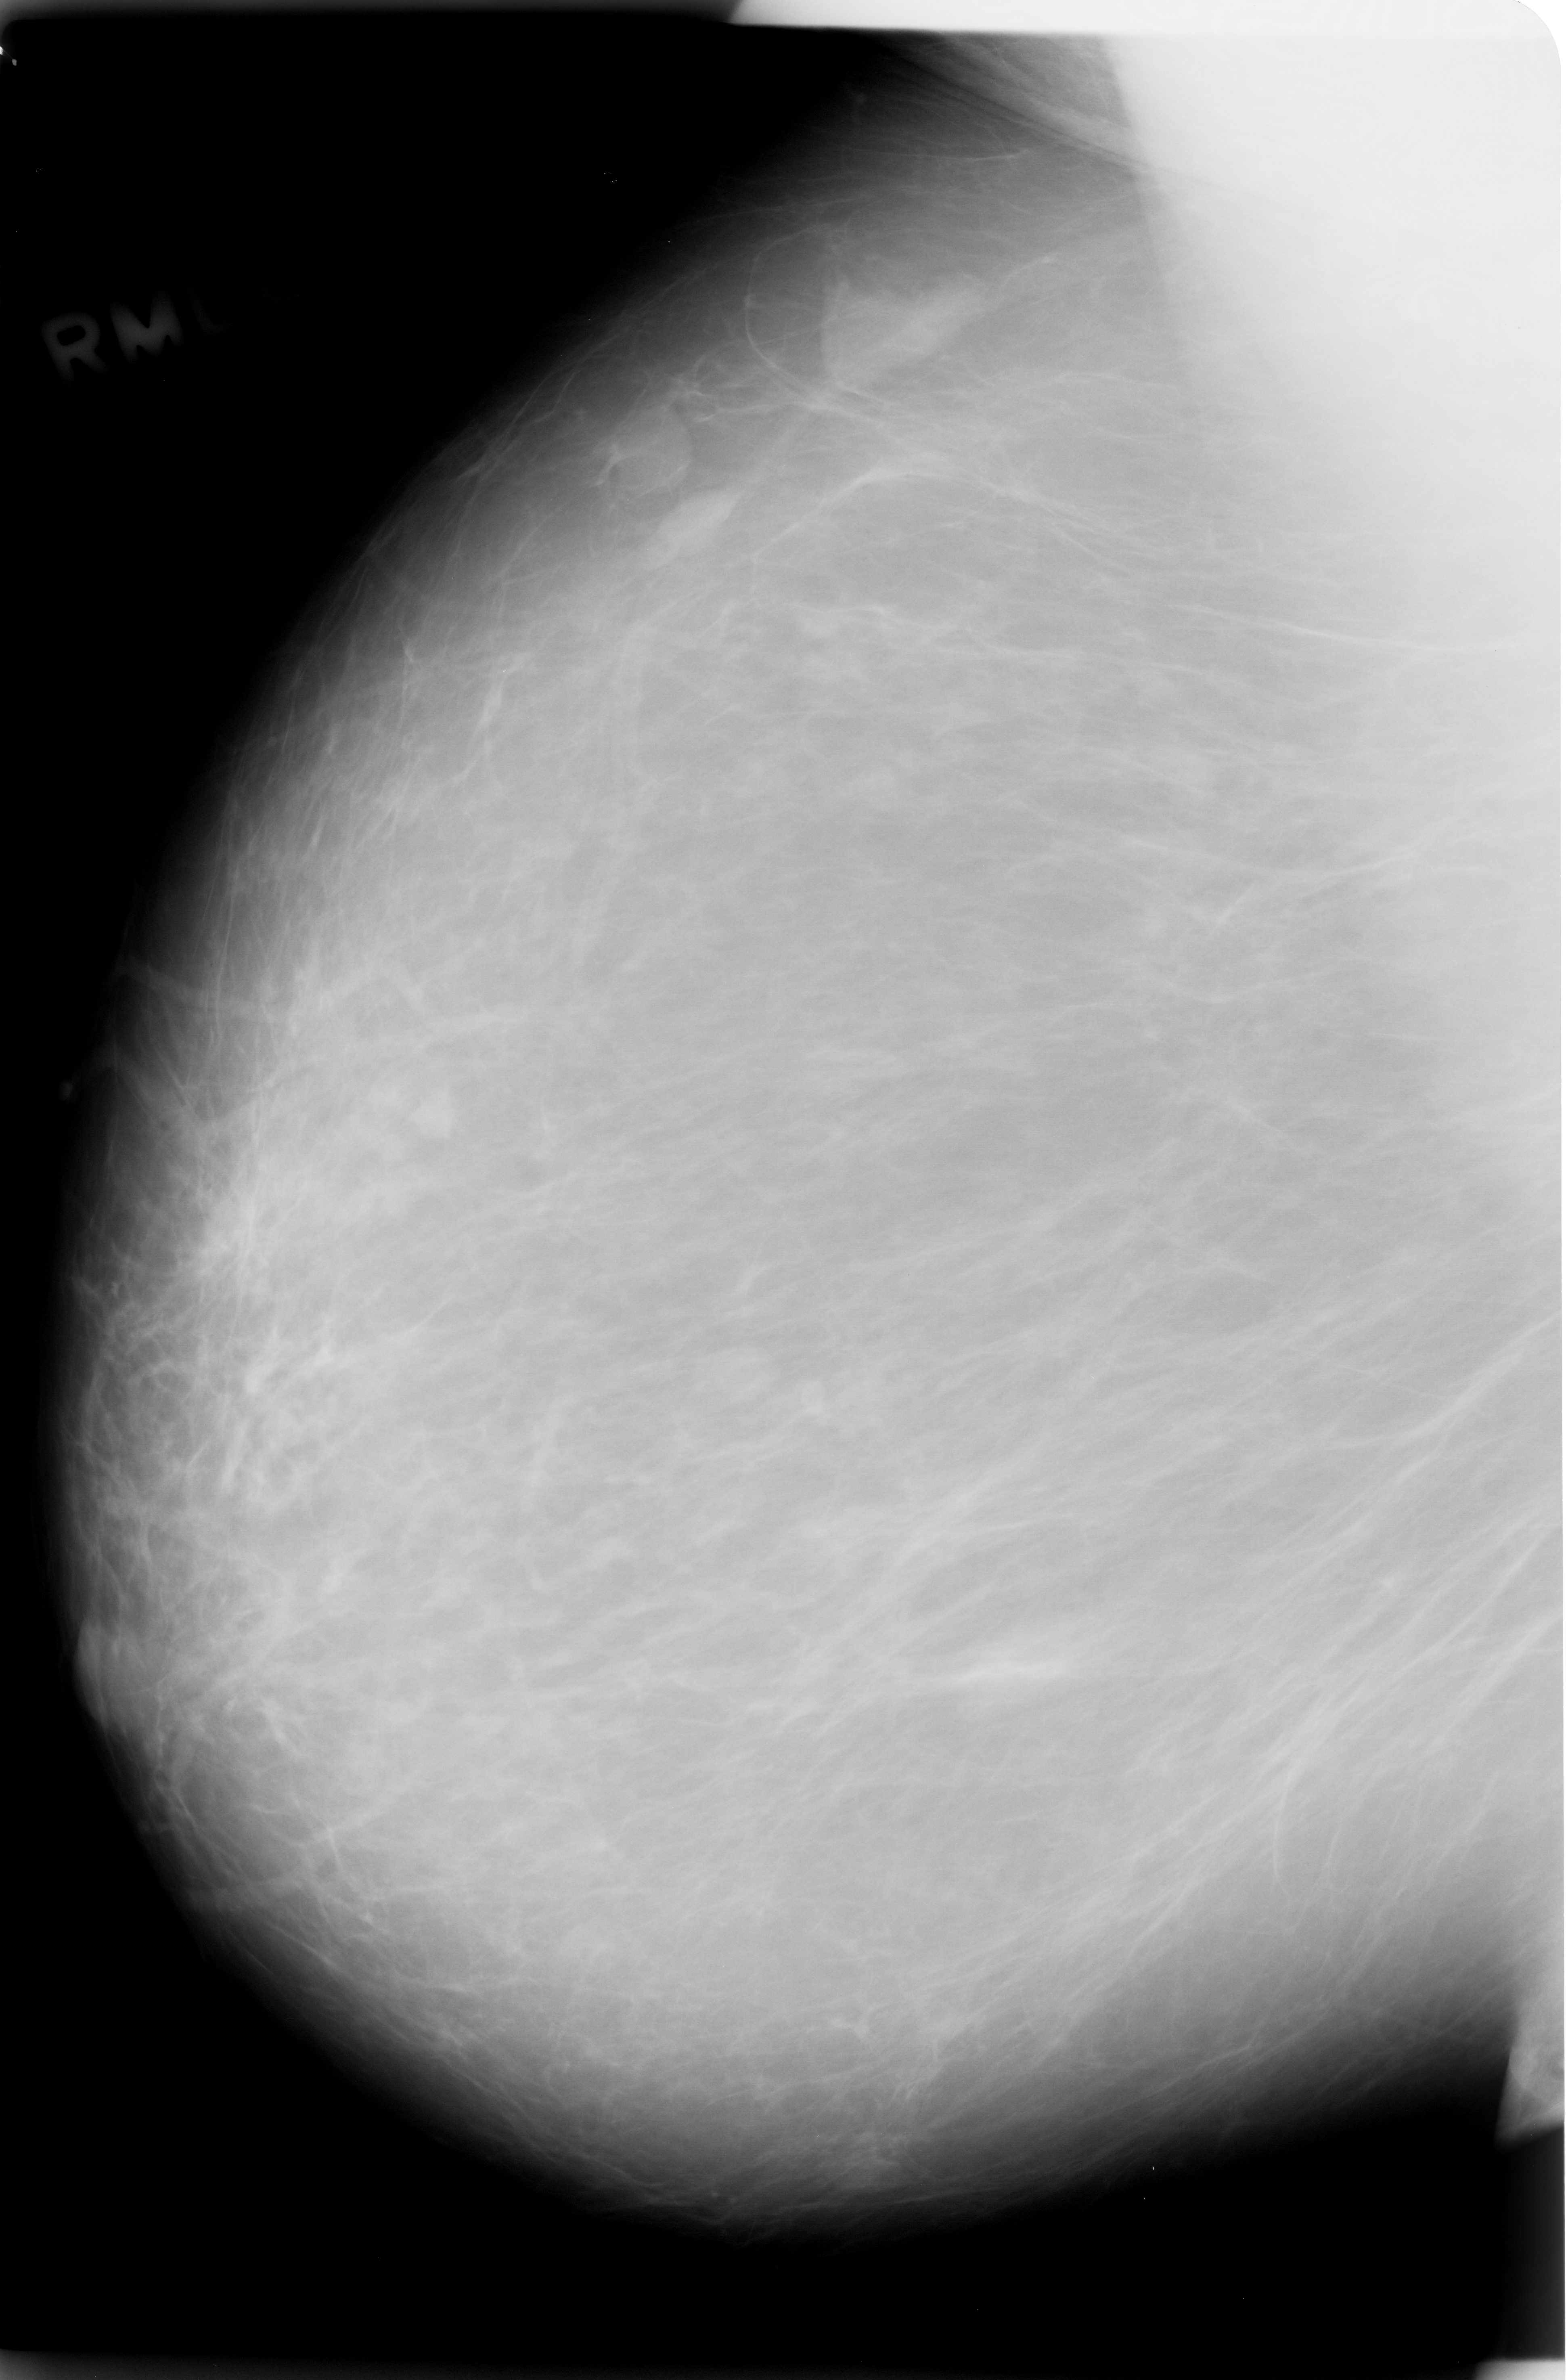
Scanned film-screen mammogram; right breast; mediolateral oblique (MLO) view; BI-RADS breast density category 1 (scale 1–4).
- Abnormality record for this image: Finding 1 of 6: mass, shape round, margins circumscribed; BI-RADS assessment category 2; pathology (as recorded): benign.
- Finding 2 of 6: mass, shape round, margins circumscribed; BI-RADS assessment category 2; pathology result (as recorded, not read from the image): benign.
- Finding 3 of 6: mass, shape round, margins circumscribed; BI-RADS assessment category 2; subtlety rating 5 on a 1 (subtle) to 5 (obvious) scale; pathology (as recorded): benign.
- Finding 4 of 6: mass, shape round, margins circumscribed; BI-RADS assessment category 2; subtlety rating 5 on a 1 (subtle) to 5 (obvious) scale; pathology result (as recorded, not read from the image): benign.
- Finding 5 of 6: mass, shape round, margins circumscribed; BI-RADS assessment category 2; pathology result (as recorded, not read from the image): benign.
- Finding 6 of 6: mass, shape round, margins circumscribed; BI-RADS assessment category 2; subtlety rating 5 on a 1 (subtle) to 5 (obvious) scale; pathology (as recorded): benign.